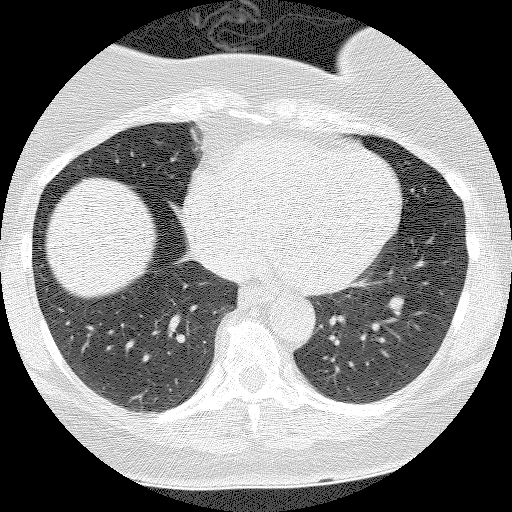
Axial slice from a low-dose chest CT screening exam, first (baseline) screen, lung window (W 1500 / L -600 HU), 2.5 mm slice thickness, lung (sharp) reconstruction kernel (BONE), slice 90 of 135 in the series. Female participant, aged 55 years at enrolment.
- Expert-annotated lung lesion, bounding box <372,286,419,327> (left, top, right, bottom; pixels).
- The screening reader recorded 3 non-calcified nodules or masses ≥4 mm on this exam (left lower lobe, right lower lobe, right lower lobe); which of them this box marks is not recorded.
- Lung cancer was diagnosed 1026 days after this screen (after the third annual screen): carcinoid tumor, NOS, left lower lobe, carcinoid, stage not assessed, 10 mm at pathology.